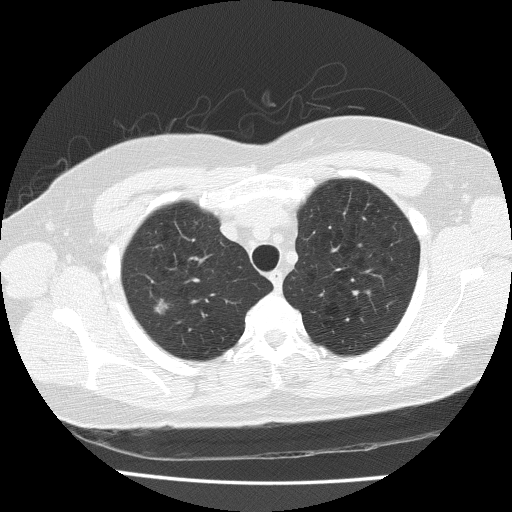
Low-dose screening chest CT, axial slice, first (baseline) screen, lung window (W 1500 / L -600 HU), lung (sharp) reconstruction kernel (FC51). Female, age 57 years at enrolment. Former smoker at enrolment.
Expert-annotated lung lesion, bounding box (x1, y1, x2, y2) in pixels: (137, 291, 179, 329). Reader record for this screening exam (exam-level; its link to the box is not recorded): non-calcified nodule or mass ≥4 mm, right upper lobe, 8 × 7 mm, spiculated (stellate) margins, soft tissue attenuation. Lung cancer was diagnosed 132 days after this screen: bronchiolo-alveolar adenocarcinoma, NOS, right upper lobe, well differentiated (G1), stage IA (AJCC 6th edition), 12 mm at pathology.